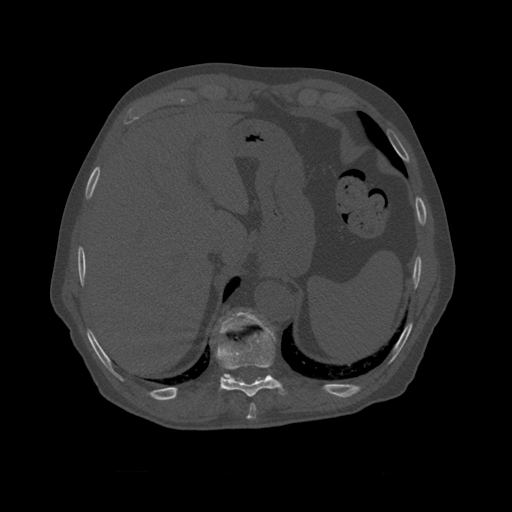
CT including the spine, one axial slice. Position 420 of 450 along the scan axis. 120 kVp. Bone window (W 1800 / L 400 HU). 512 × 512 image matrix, field of view 405 × 405 mm. Patient age 75 years. Case-level facts recorded for this patient, not image findings: primary cancer: prostate.
Outlined on this slice (semi-automatically segmented with operator editing):
- T10 vertebra: bounding box (x1, y1, x2, y2) in pixels: (215, 309, 272, 379)
- T8 vertebra: (249, 403, 257, 411)
- T9 vertebra: (216, 327, 287, 397)